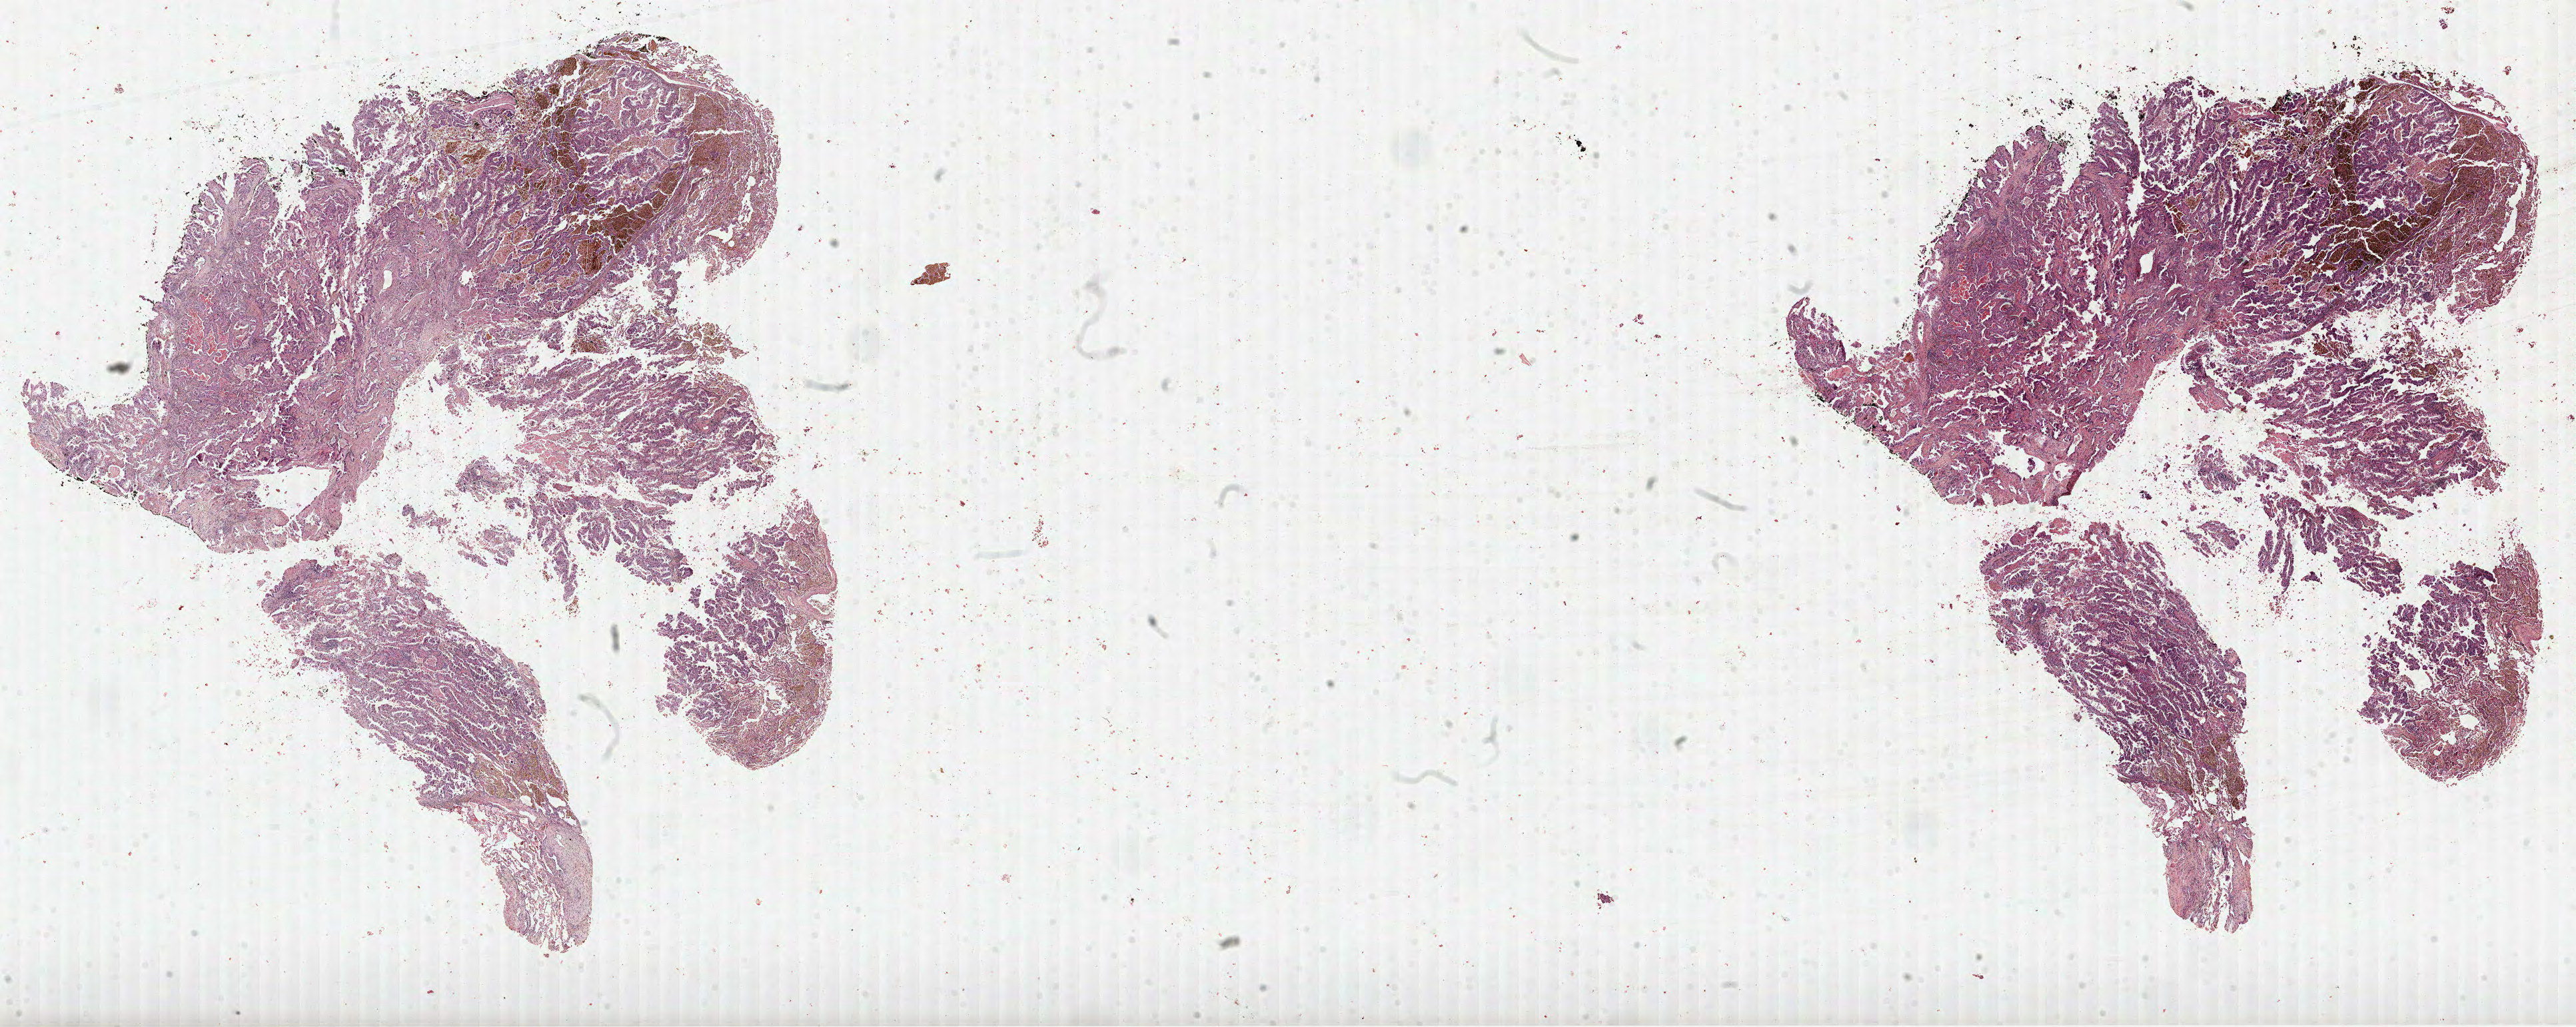
Digitized H&E-stained tissue section (whole slide), shown as a low-resolution overview of the whole scanned area (about 31.2 x 12.4 mm, acquisition: 40x scan); formalin-fixed paraffin-embedded (FFPE) diagnostic section; sample: primary tumour, lung. Male, age 65 years at initial diagnosis.
TNM: T2 N0 M0. Histologic diagnosis: Adenocarcinoma, NOS (upper lobe, lung). Laterality: left. AJCC pathologic stage: IA.